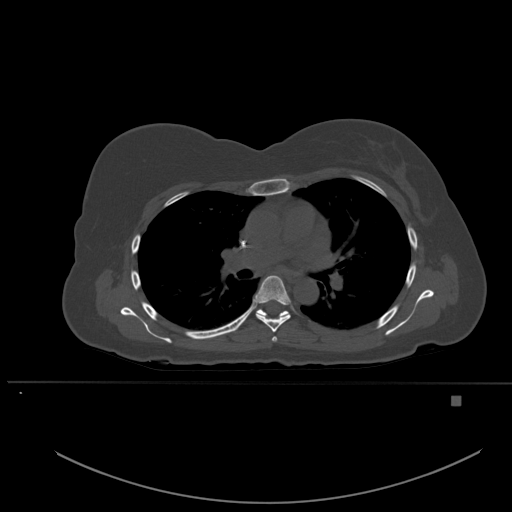
CT including the spine, one axial slice. Slice 361 of 651 in the series (ordered by position). Bone window (W 1800 / L 400 HU). 1.5 mm slice thickness. 512 × 512 image matrix, field of view 443 × 443 mm. Female patient, age 49 years. Case-level facts recorded for this patient, not image findings: primary cancer: breast; vertebrae with lytic lesions (as recorded): L3, T12, L4.
Structures marked on this image (semi-automatically segmented with operator editing):
- T4 vertebra: bounding box (x1, y1, x2, y2) in pixels: (272, 337, 277, 342)
- T5 vertebra: (255, 275, 291, 333)
- T6 vertebra: (241, 309, 290, 325)